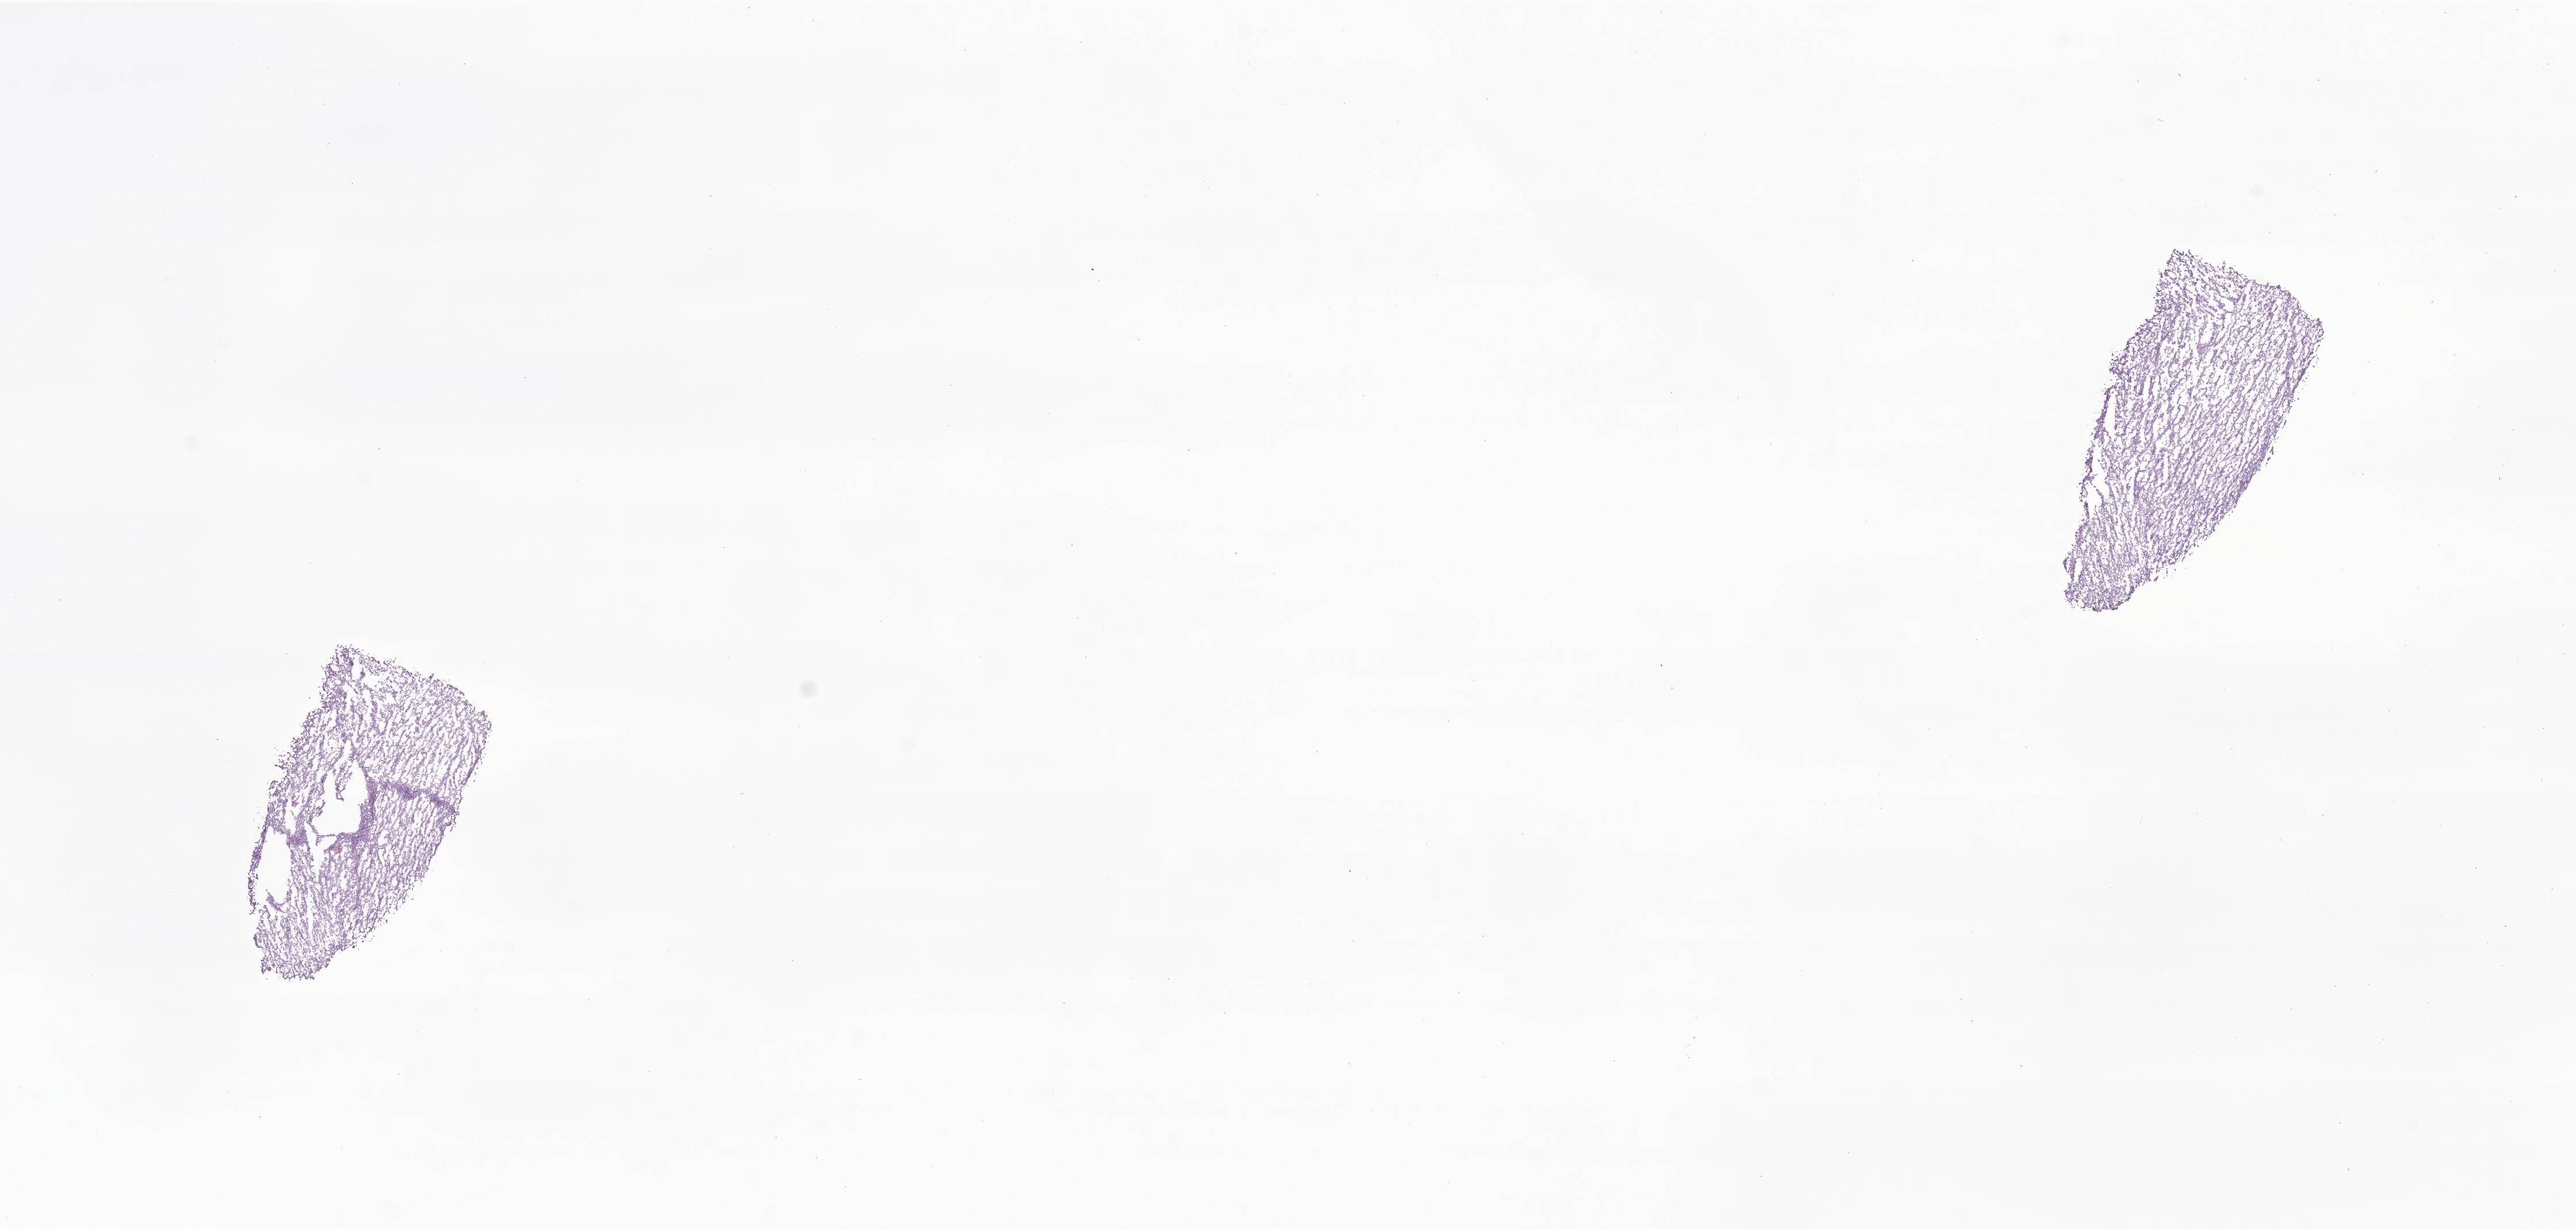
Digitized H&E-stained section of tumor tissue from the nasal cavity — whole scanned area (about 18.9 x 9.0 mm) shown as a low-resolution overview, frozen section (OCT-embedded). Female patient, age 149 months (12 years 5 months).
Diagnosis: Neoplasm, metastatic.